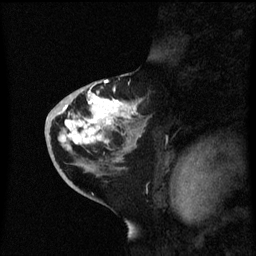
Breast MRI (dynamic contrast-enhanced), one sagittal slice; slice 32 of 60 in the series (ordered by position); dynamic contrast-enhanced series, image 2 of 3 at this slice position (ordered by acquisition); 1.5 T; TE 4.2 ms, TR 8.4 ms; 2.3 mm slice thickness; 256 × 256 image matrix, field of view 200 × 200 mm. Female patient, age 46 years. Case-level facts recorded for this patient, not image findings: setting: breast cancer imaged before/during neoadjuvant chemotherapy; receptor status: HER2-positive.
Outlined on this slice (semi-automatically segmented with operator editing):
- analysis volume of interest (the breast-tissue region the enhancement analysis was run in; not a lesion): bounding box (x1, y1, x2, y2) in pixels: (46, 86, 151, 171)
- tumour enhancement mask (voxels above the 70 % enhancement threshold inside the analysis volume of interest): (58, 92, 135, 149)